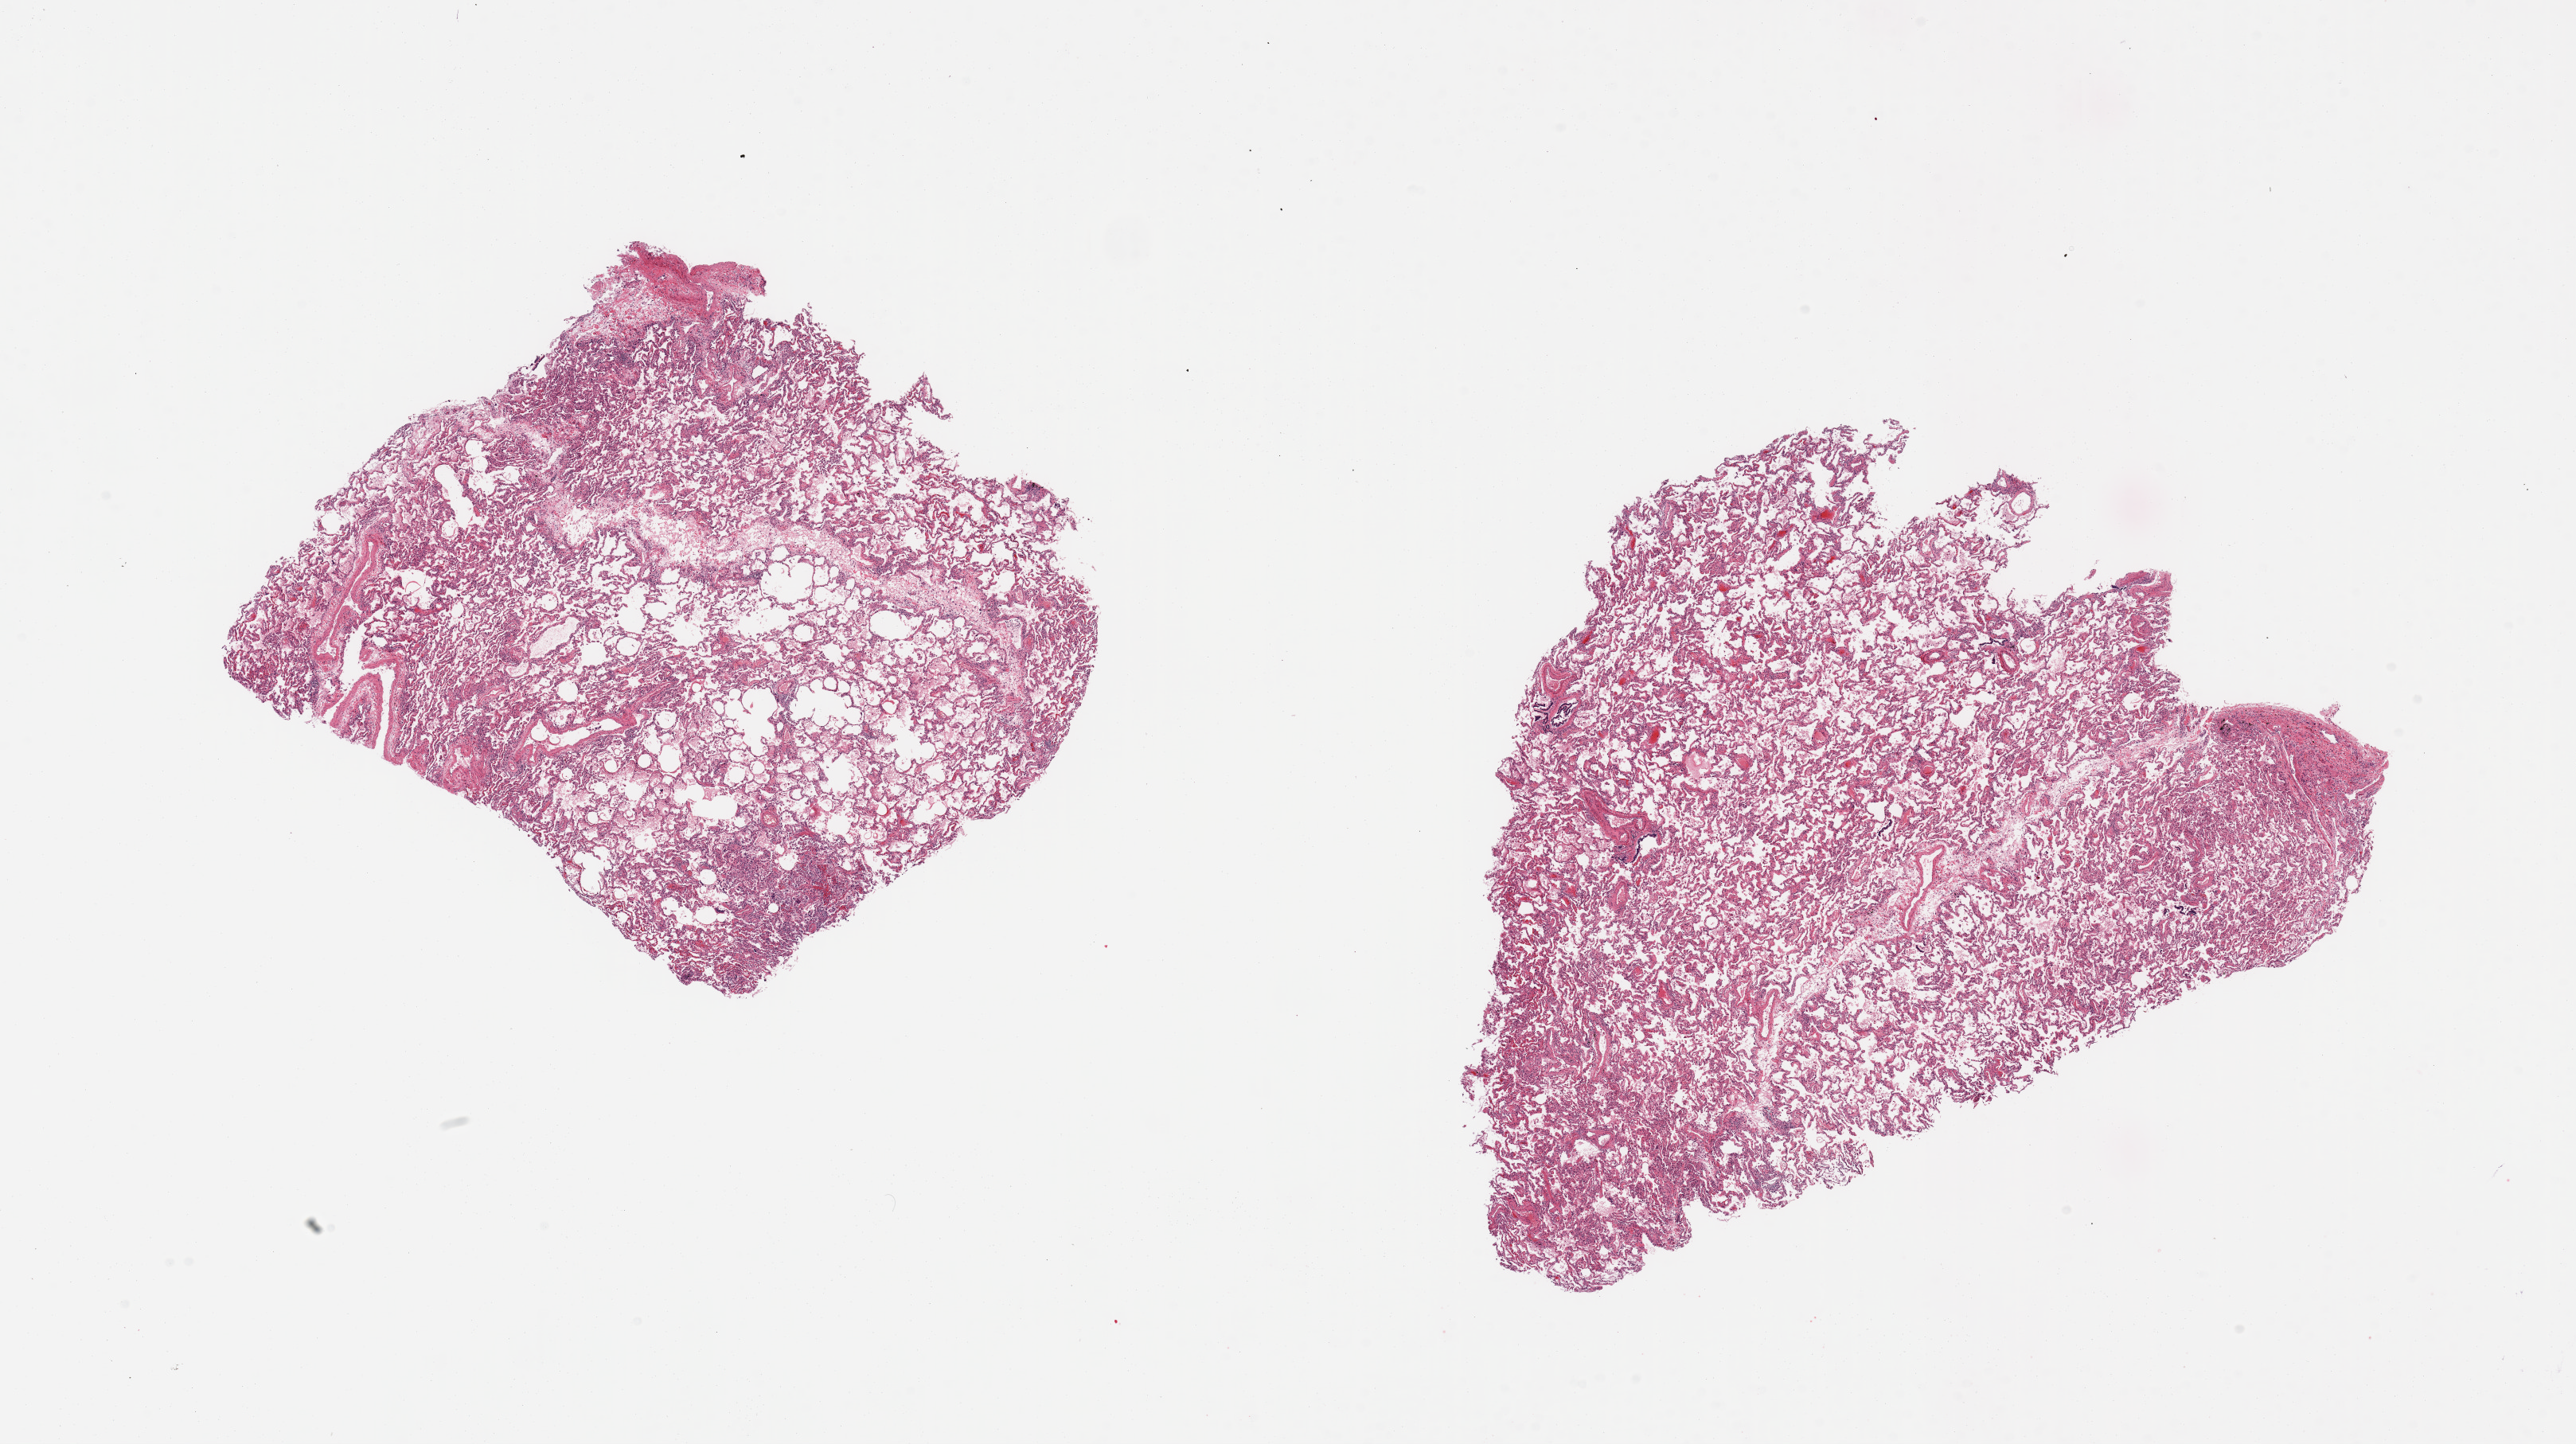
Whole-slide image, H&E stain, low-resolution overview of the scanned area, about 25.6 x 14.3 mm; PAXgene-fixed paraffin-embedded (PFPE) section; target tissue: lung; donor tissue sample. Male donor.
Reviewer comment on this tissue sample: 2 pieces.